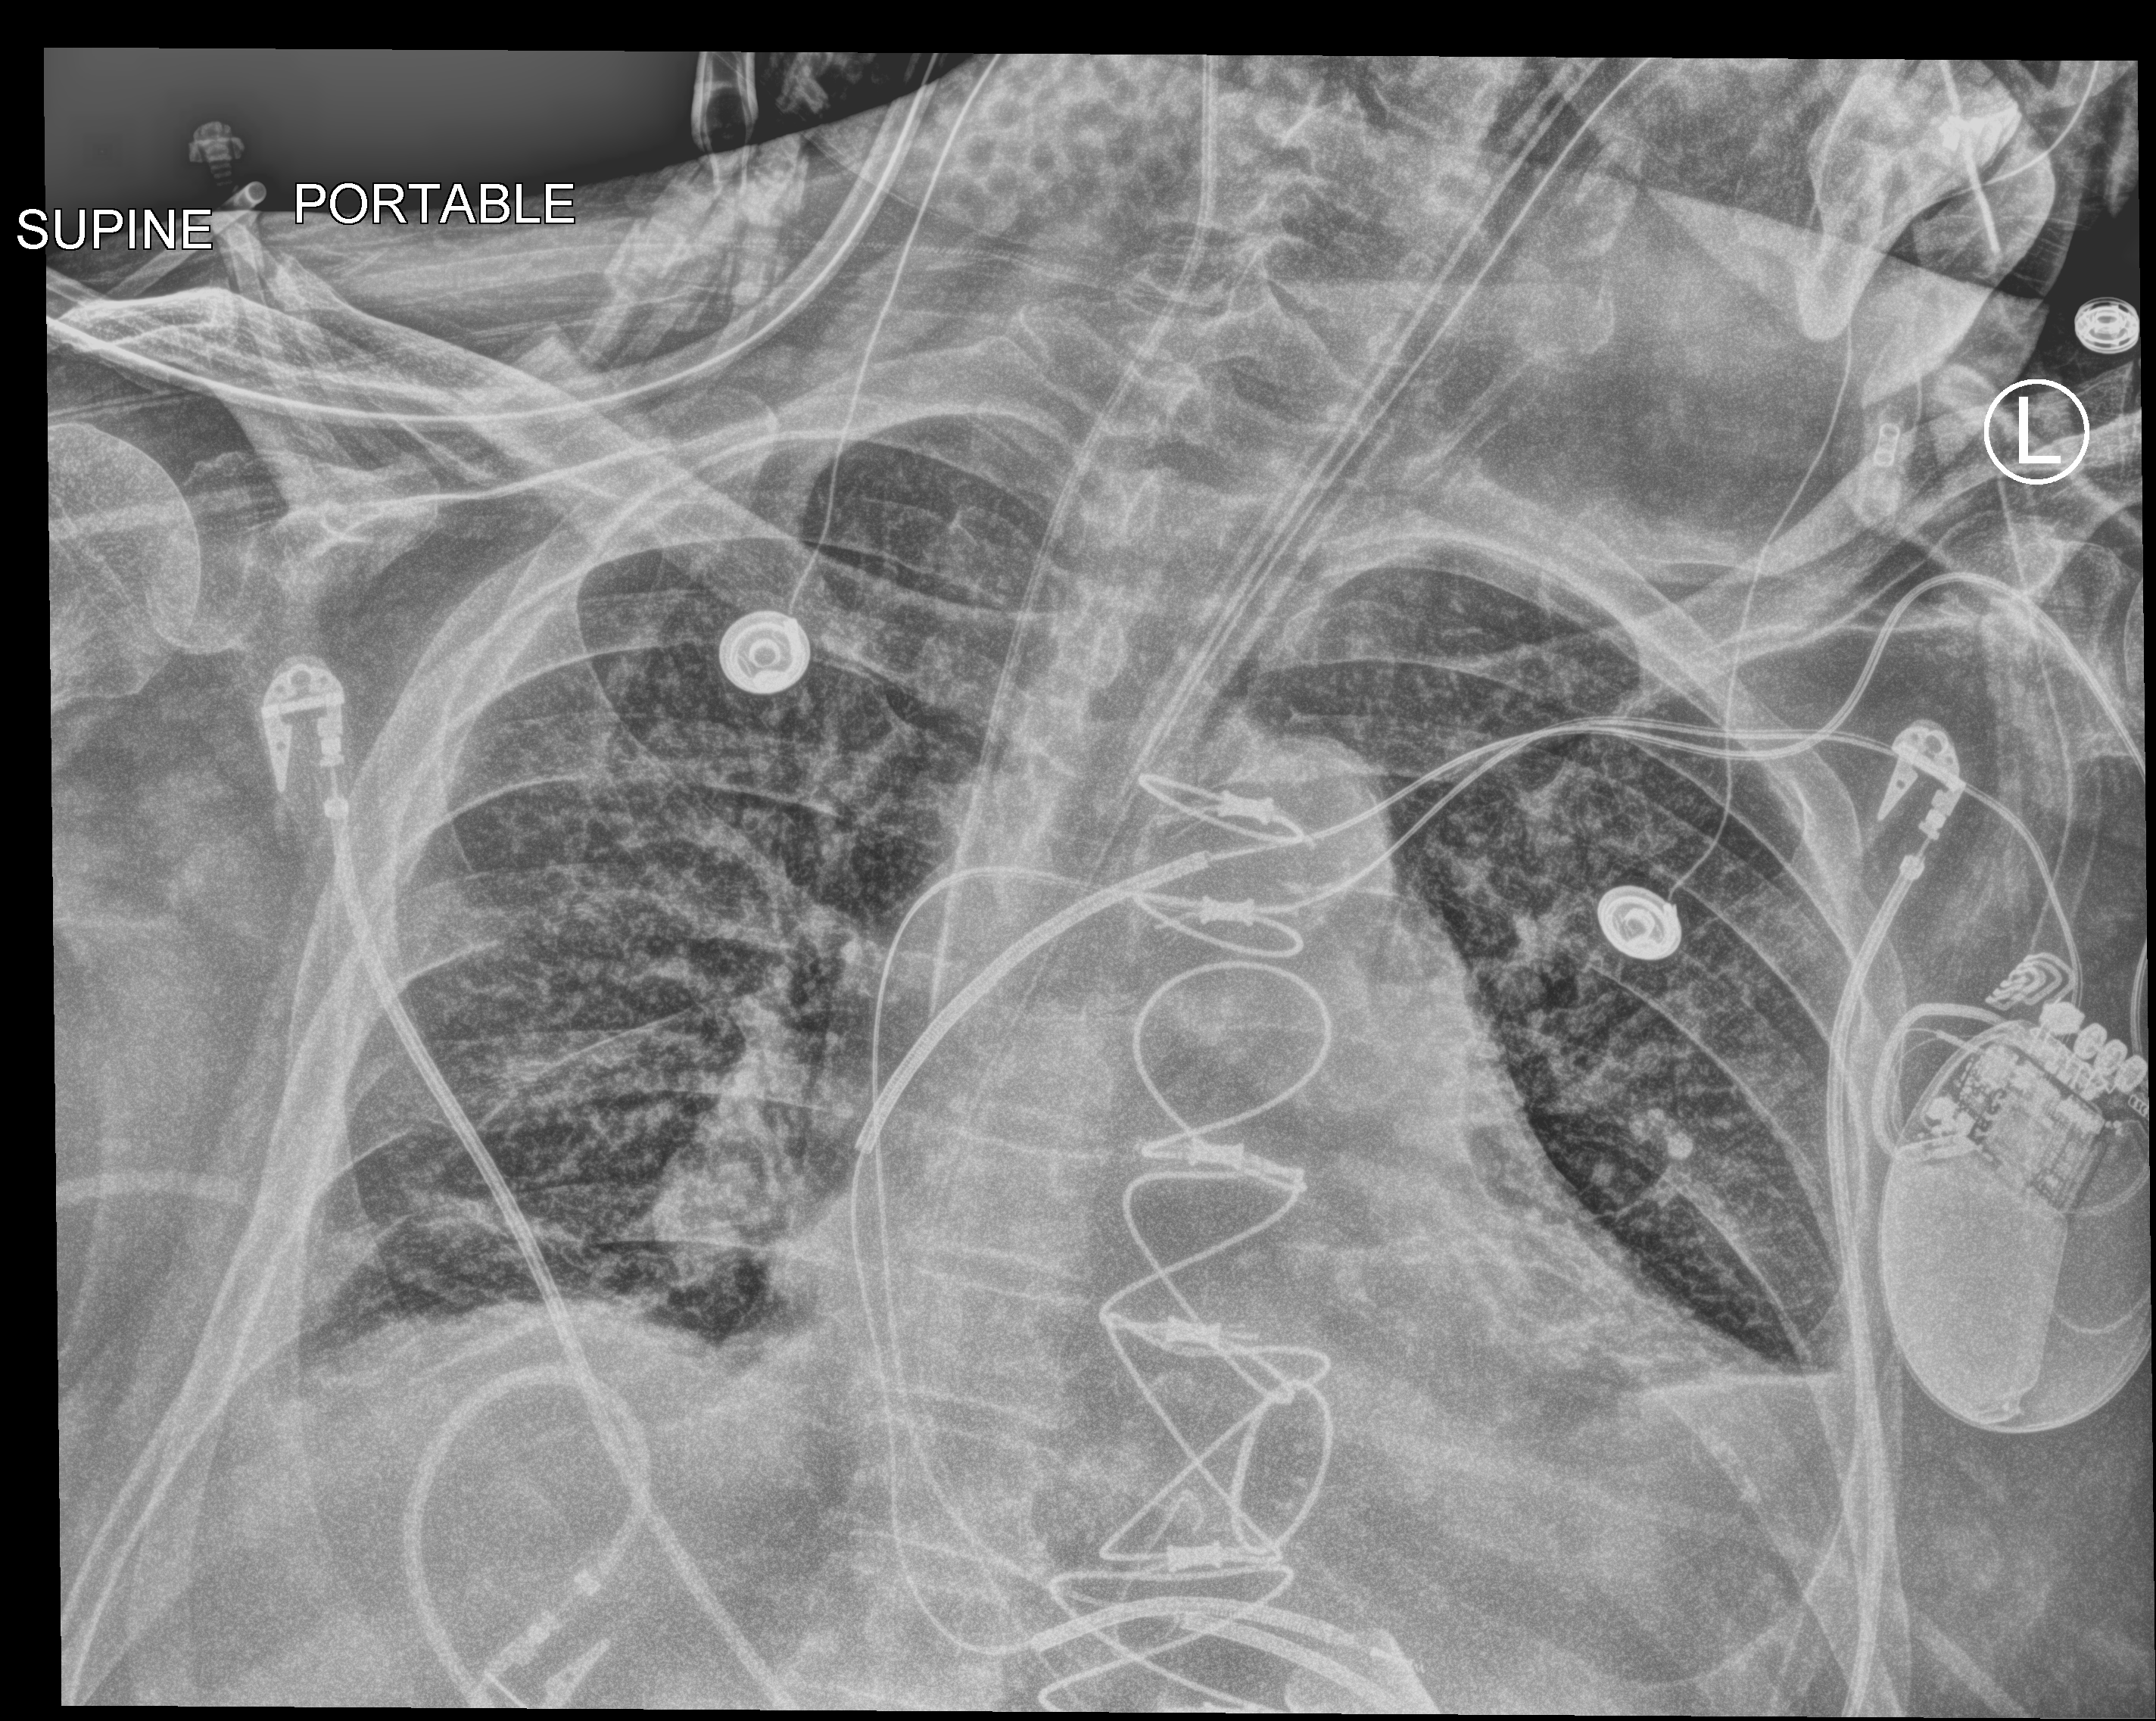
Portable chest radiograph. Male patient hospitalised with COVID-19, age 60–74 years.
From the hospital-stay record, not from the radiograph (when in the stay this image was taken is not recorded): COPD (admission record): no; hypertension (admission record): yes; mechanically ventilated during this hospital stay: no.